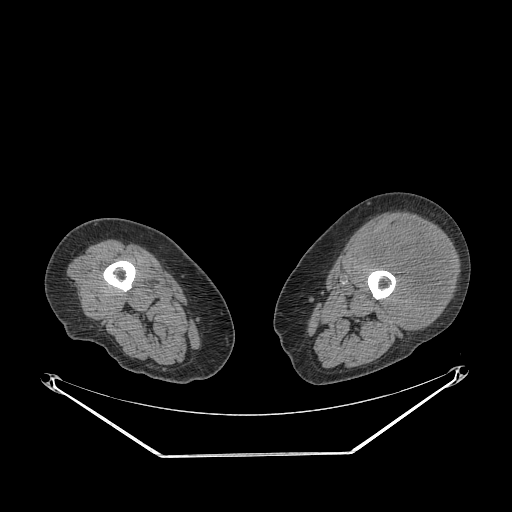
CT of an extremity soft-tissue mass (from a PET/CT study), one axial slice. Position 215 of 267 along the scan axis. Reconstruction kernel STANDARD. 140 kVp. Soft-tissue window (W 400 / L 40 HU). 512 × 512 image matrix. Female patient. From the clinical record (not read from this slice): histological type: undifferentiated – high grade; grade: high; site of the primary tumour: left thigh.
Outlined on this slice (expert contour drawn on MRI and transferred to this co-registered scan by the dataset authors):
- gross tumour volume including surrounding oedema: bounding box (x1, y1, x2, y2) in pixels: (361, 224, 451, 330)
- gross tumour volume (mass): (363, 224, 451, 330)